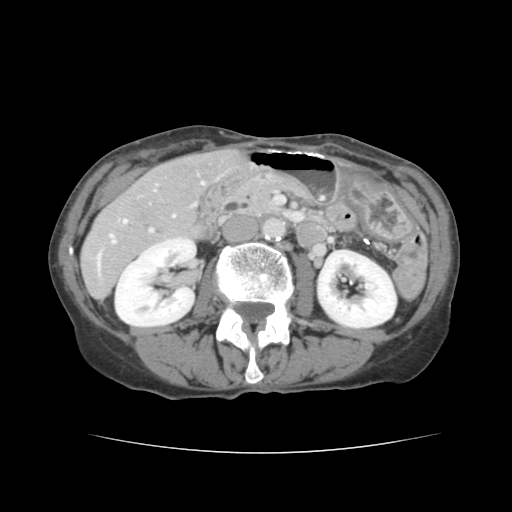
Contrast-enhanced abdominal CT, one axial slice. Slice 54 of 136 in the series (ordered by position). 120 kVp. Soft-tissue window (W 400 / L 40 HU). 2.5 mm slice thickness. 512 × 512 image matrix, field of view 319 × 319 mm. Female patient, age 77 years. Case-level facts recorded for this patient, not image findings: diagnosis: colorectal cancer liver metastases, imaged before liver resection; multiple liver metastases: yes; largest metastasis: 3 cm; chemotherapy before resection: yes.
Outlined on this slice (outlined manually by an expert reader):
- hepatic veins: bounding box [x1, y1, x2, y2] px = [110, 182, 204, 243]
- liver: [82, 149, 241, 300]
- planned liver remnant (the part of the liver to remain after resection): [167, 150, 242, 194]
- portal vein (with intrahepatic branches): [97, 229, 153, 272]